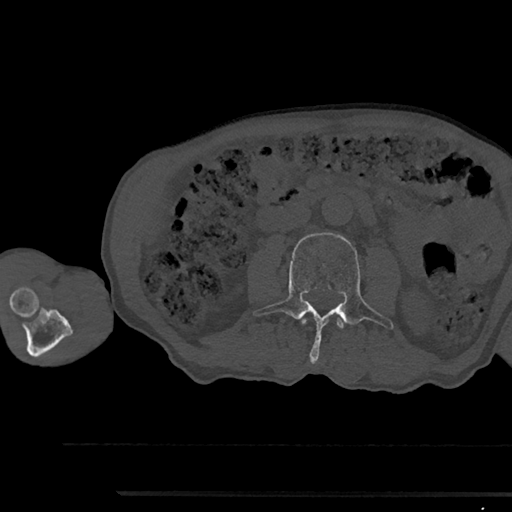
CT including the spine, one axial slice; position 499 of 797 along the scan axis; 120 kVp; bone window (W 1800 / L 400 HU); 512 × 512 image matrix, field of view 367 × 367 mm. Male patient, age 79 years. From the clinical record (not read from this slice): primary cancer: prostate.
Structures marked on this image (semi-automatically segmented with operator editing):
- L2 vertebra: box from (x=302, y=319) to (x=343, y=329) px
- L3 vertebra: (x=253, y=233)–(x=393, y=363)